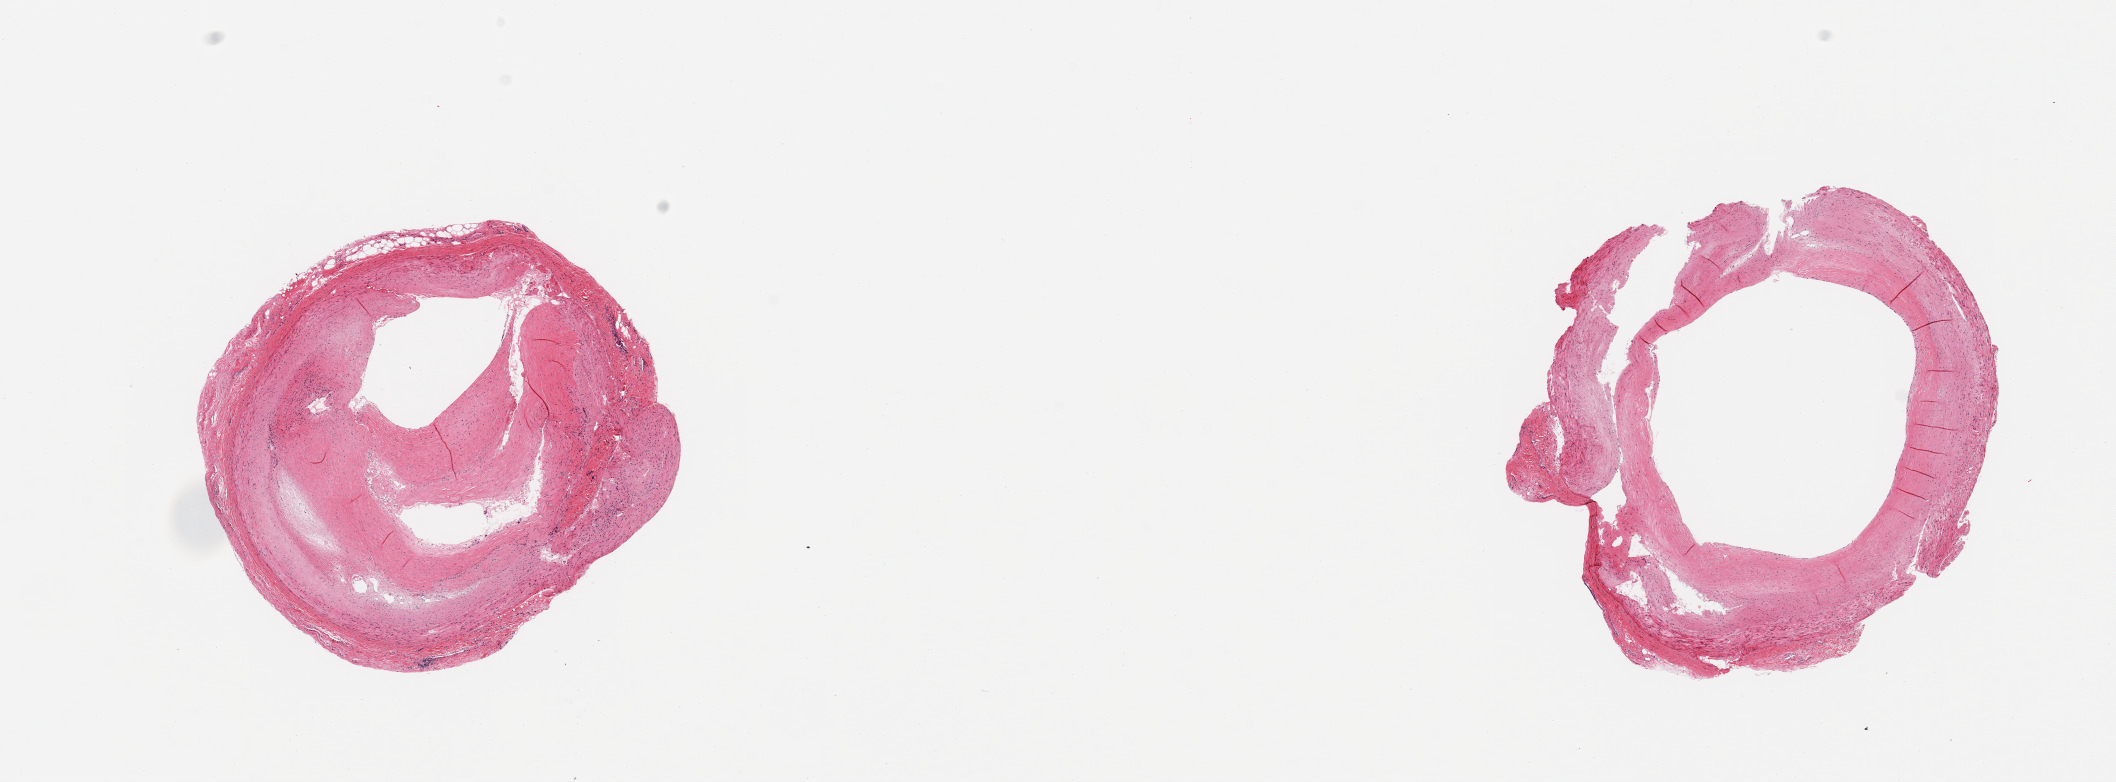
Hematoxylin and eosin (H&E) whole-slide image — low-resolution overview of the scanned area, about 16.7 x 6.2 mm (from a 20x scan); PAXgene-fixed paraffin-embedded (PFPE) section; section of coronary artery (target tissue); tissue donor sample. Female donor.
Reviewer comment on this tissue sample: 2 pieces: 1 with 75% occlusion with eccentric plaque; other has concentric plaque.